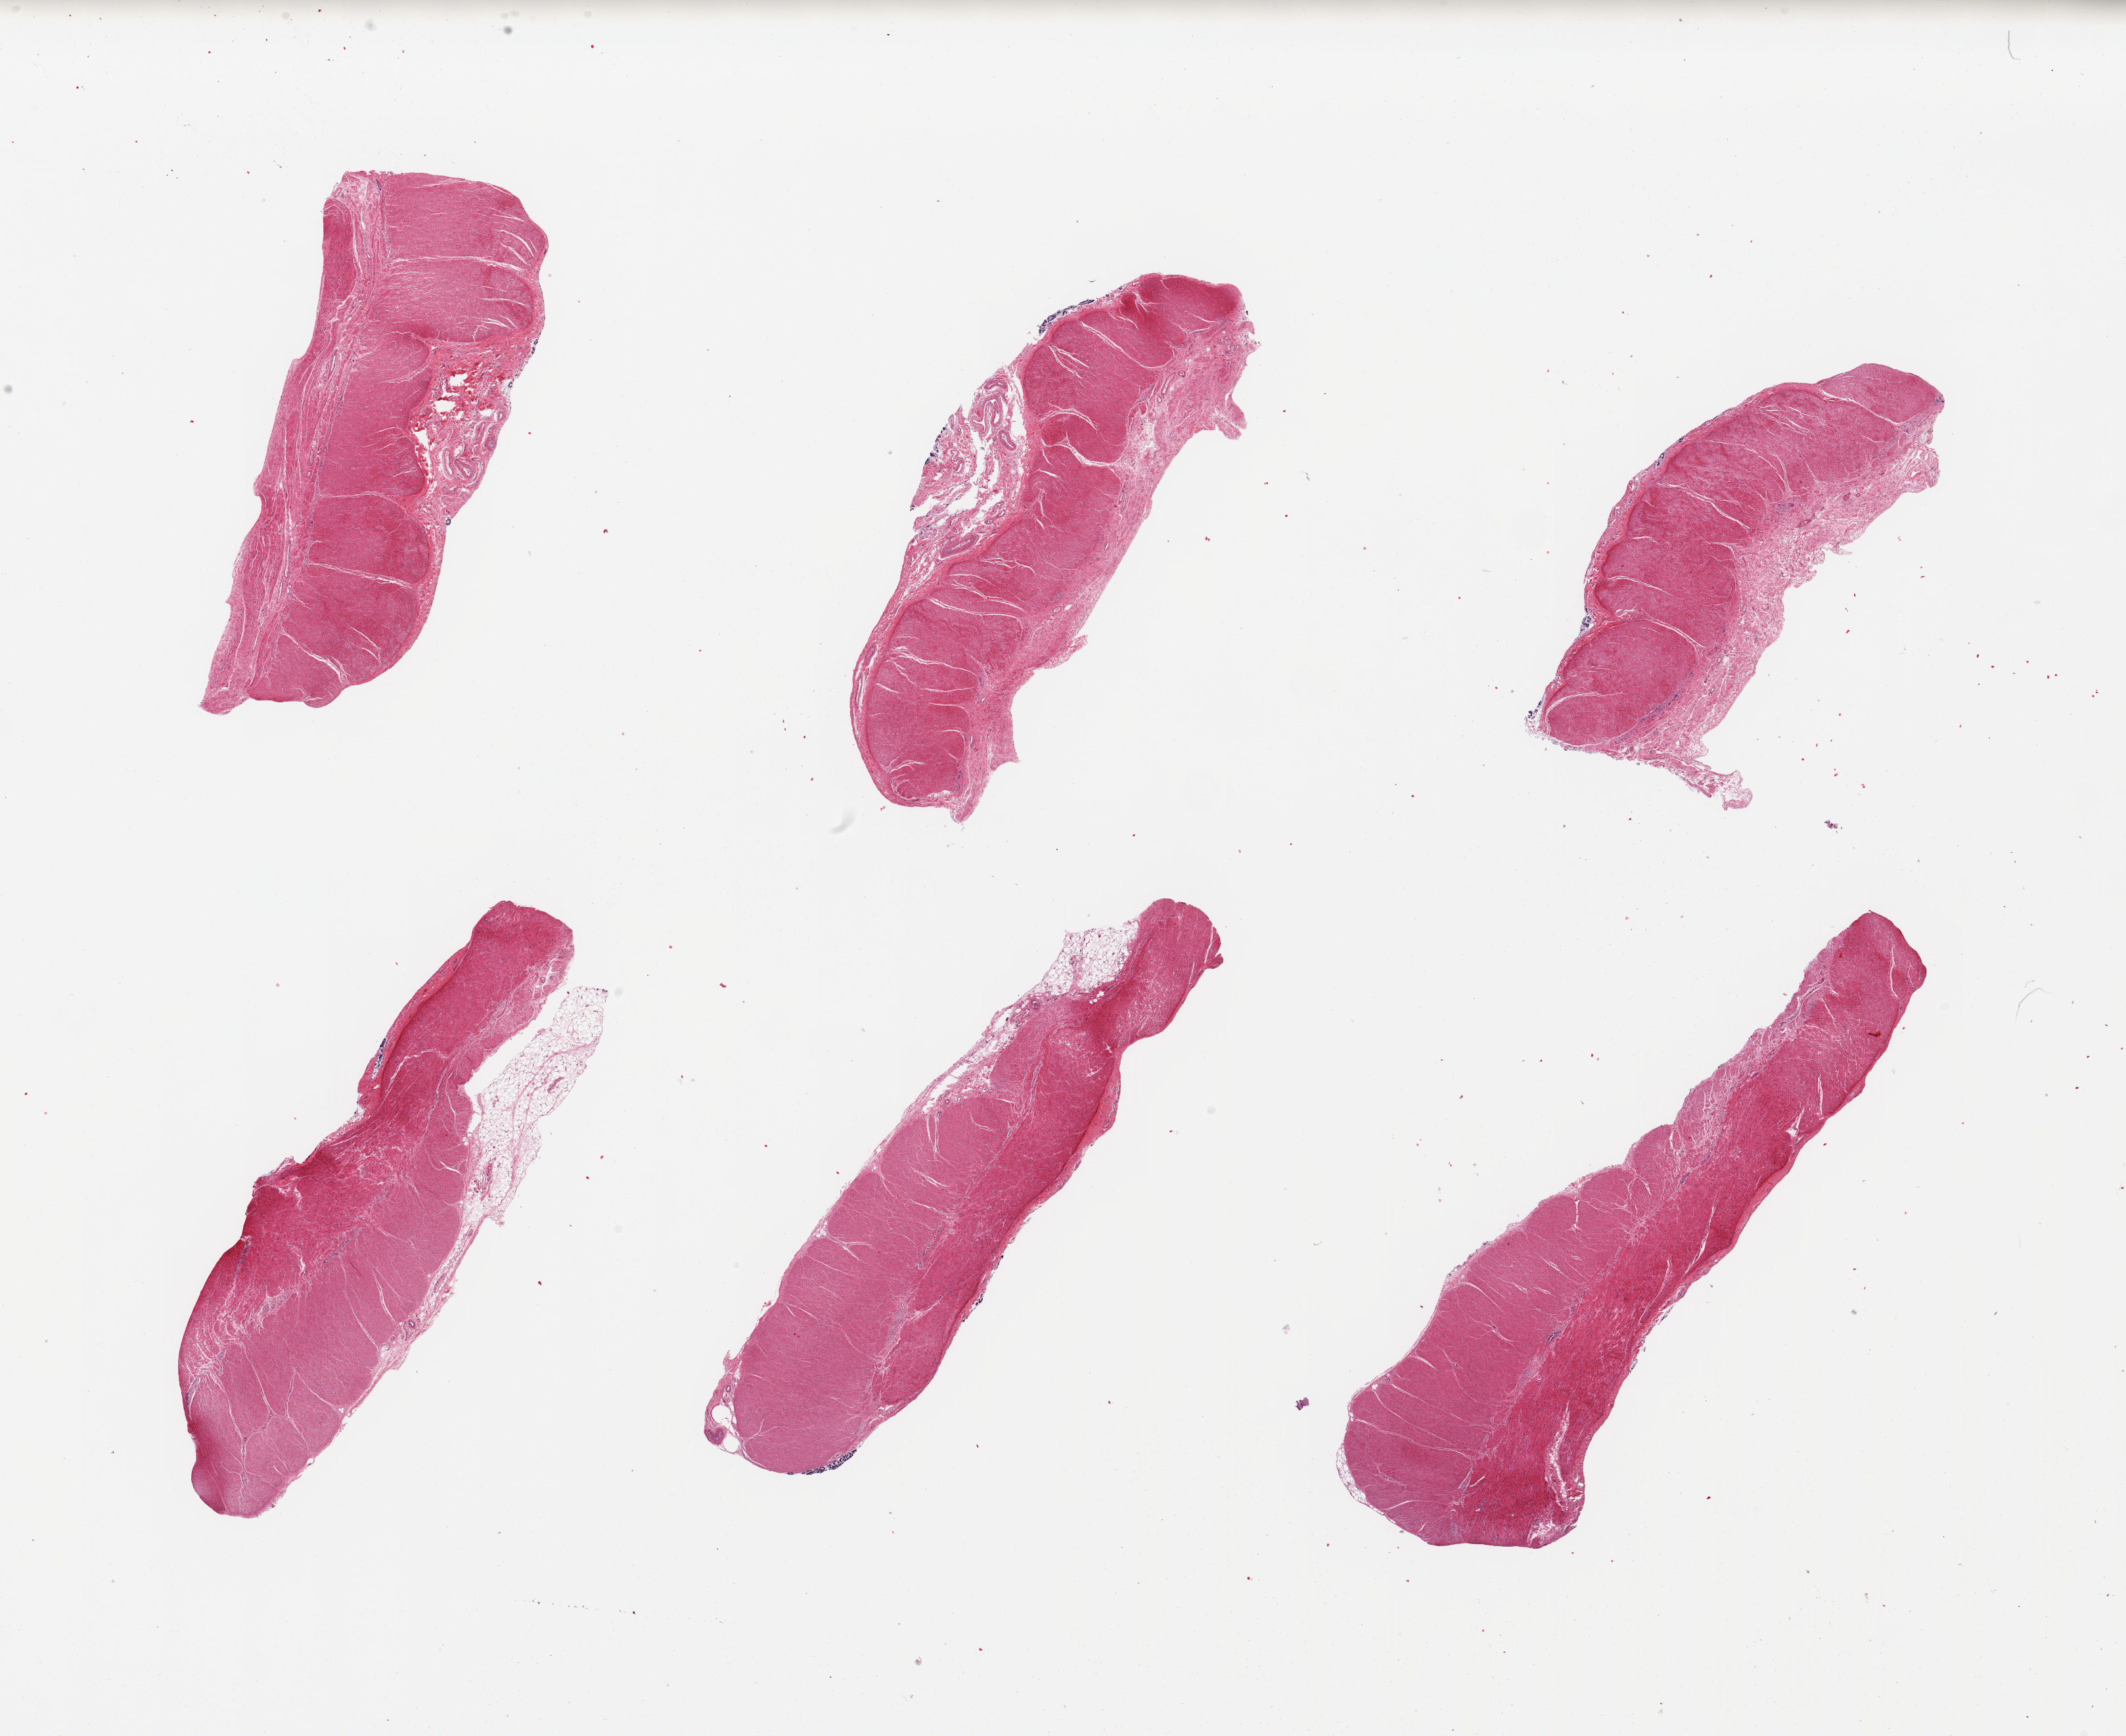
Hematoxylin and eosin (H&E) whole-slide image — a low-resolution overview of the entire scanned area, about 25.6 x 20.9 mm (slide scanned at 20x); PAXgene-fixed paraffin-embedded (PFPE) section; target tissue: sigmoid colon; tissue donor sample.
Reviewer comment on this tissue sample: 6 pieces; target muscularis with partial rim of submucosa/serosa.